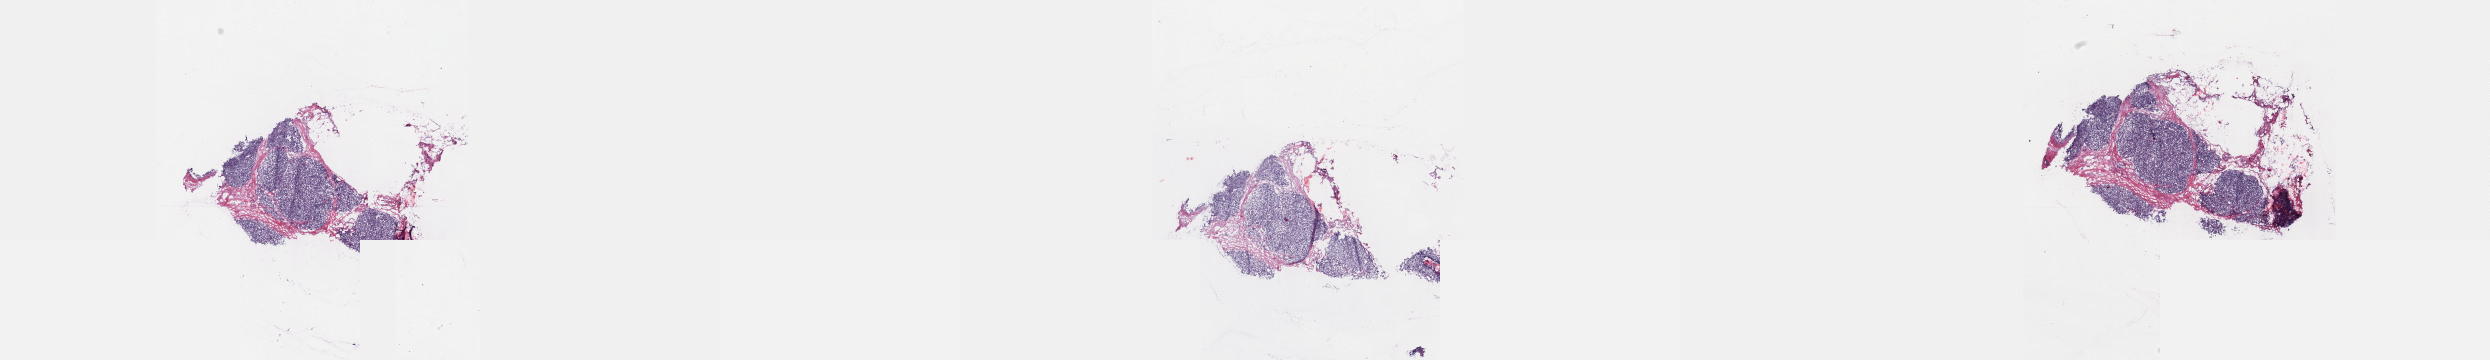
H&E whole-slide image — a low-resolution overview of the entire scanned area, about 40.2 x 5.8 mm (slide scanned at 40x), frozen section from the top of the tissue portion, thymus, primary tumour sample. Patient: female, age at initial diagnosis 61 years.
Pathologic diagnosis: Thymoma, type B2, NOS.